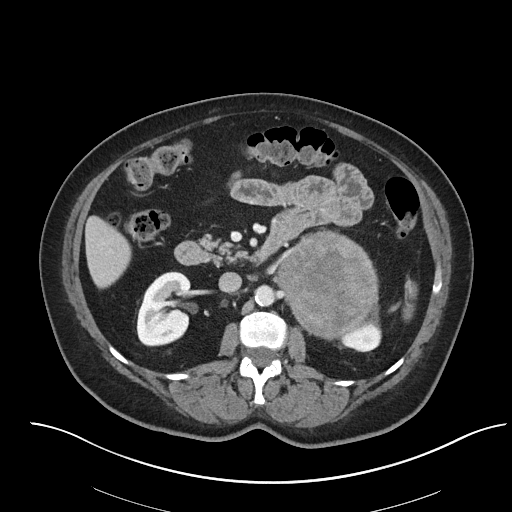
Contrast-enhanced abdominal CT, one axial slice; slice 35 of 92 in the series (ordered by position); 120 kVp; intravenous contrast given; soft-tissue window (W 400 / L 40 HU); 3 mm slice thickness; 512 × 512 image matrix, field of view 440 × 440 mm. Female patient, age 53 years. From the clinical record (not read from this slice): diagnosis: adrenocortical carcinoma; tumour side: left adrenal; tumour size at pathology: 9 cm; Ki-67 index: 28 %; stage (as recorded): 2.
Outlined on this slice (semi-automatic segmentation, software-assisted and operator-edited):
- mass: bounding box (x1, y1, x2, y2) in pixels: (279, 233, 377, 338)